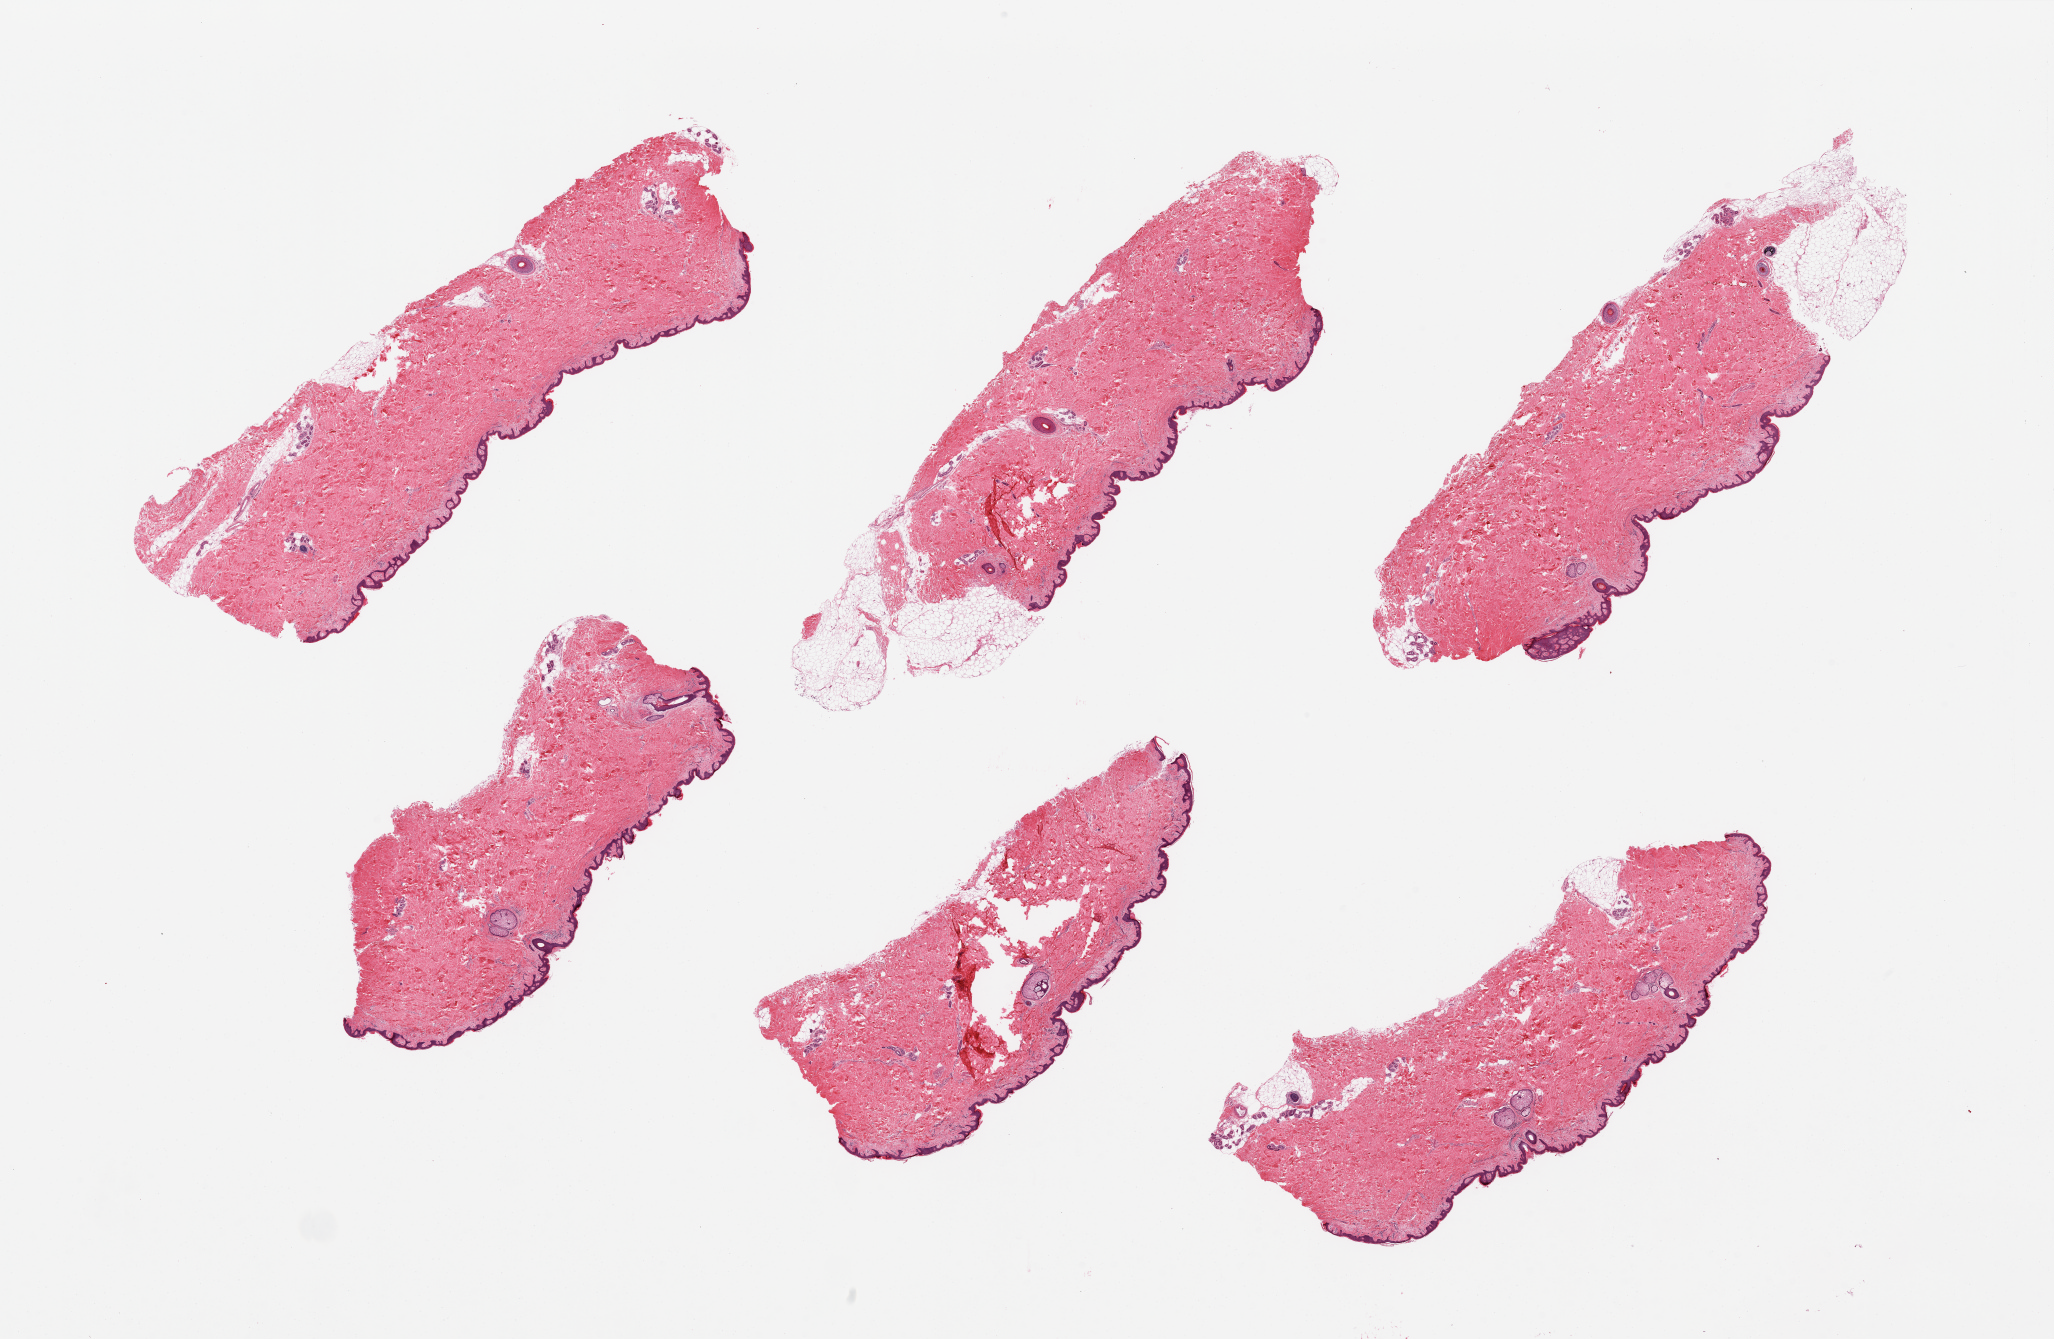
Haematoxylin and eosin whole-slide image, brightfield — low-resolution overview of the scanned area, about 32.5 x 21.2 mm (from a 20x scan), PAXgene-fixed, paraffin-embedded tissue, sampled site (target tissue): skin of suprapubic region, tissue donor sample. Male donor.
* reviewer comment on this tissue sample: 6 pieces, 2 with ~20% attached fat